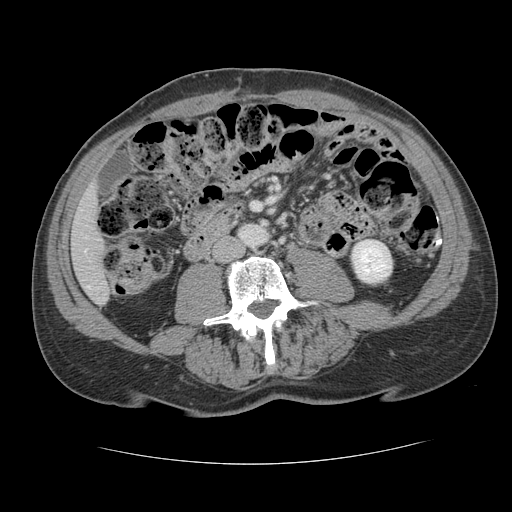
Contrast-enhanced abdominal CT, one axial slice. Slice 28 of 134 in the series (ordered by position). 120 kVp. Intravenous contrast given. Soft-tissue window (W 400 / L 40 HU). 2.5 mm slice thickness. 512 × 512 image matrix. Male patient, age 68 years. Case-level facts recorded for this patient, not image findings: diagnosis: colorectal cancer liver metastases, imaged before liver resection; multiple liver metastases: yes; largest metastasis: 2.2 cm; disease in both lobes: no.
Annotated regions visible in this slice (manually delineated by an expert):
- liver: bounding box [x1, y1, x2, y2] px = [72, 188, 110, 303]
- planned liver remnant (the part of the liver to remain after resection): [72, 189, 110, 303]
- portal vein (with intrahepatic branches): [87, 286, 89, 288]